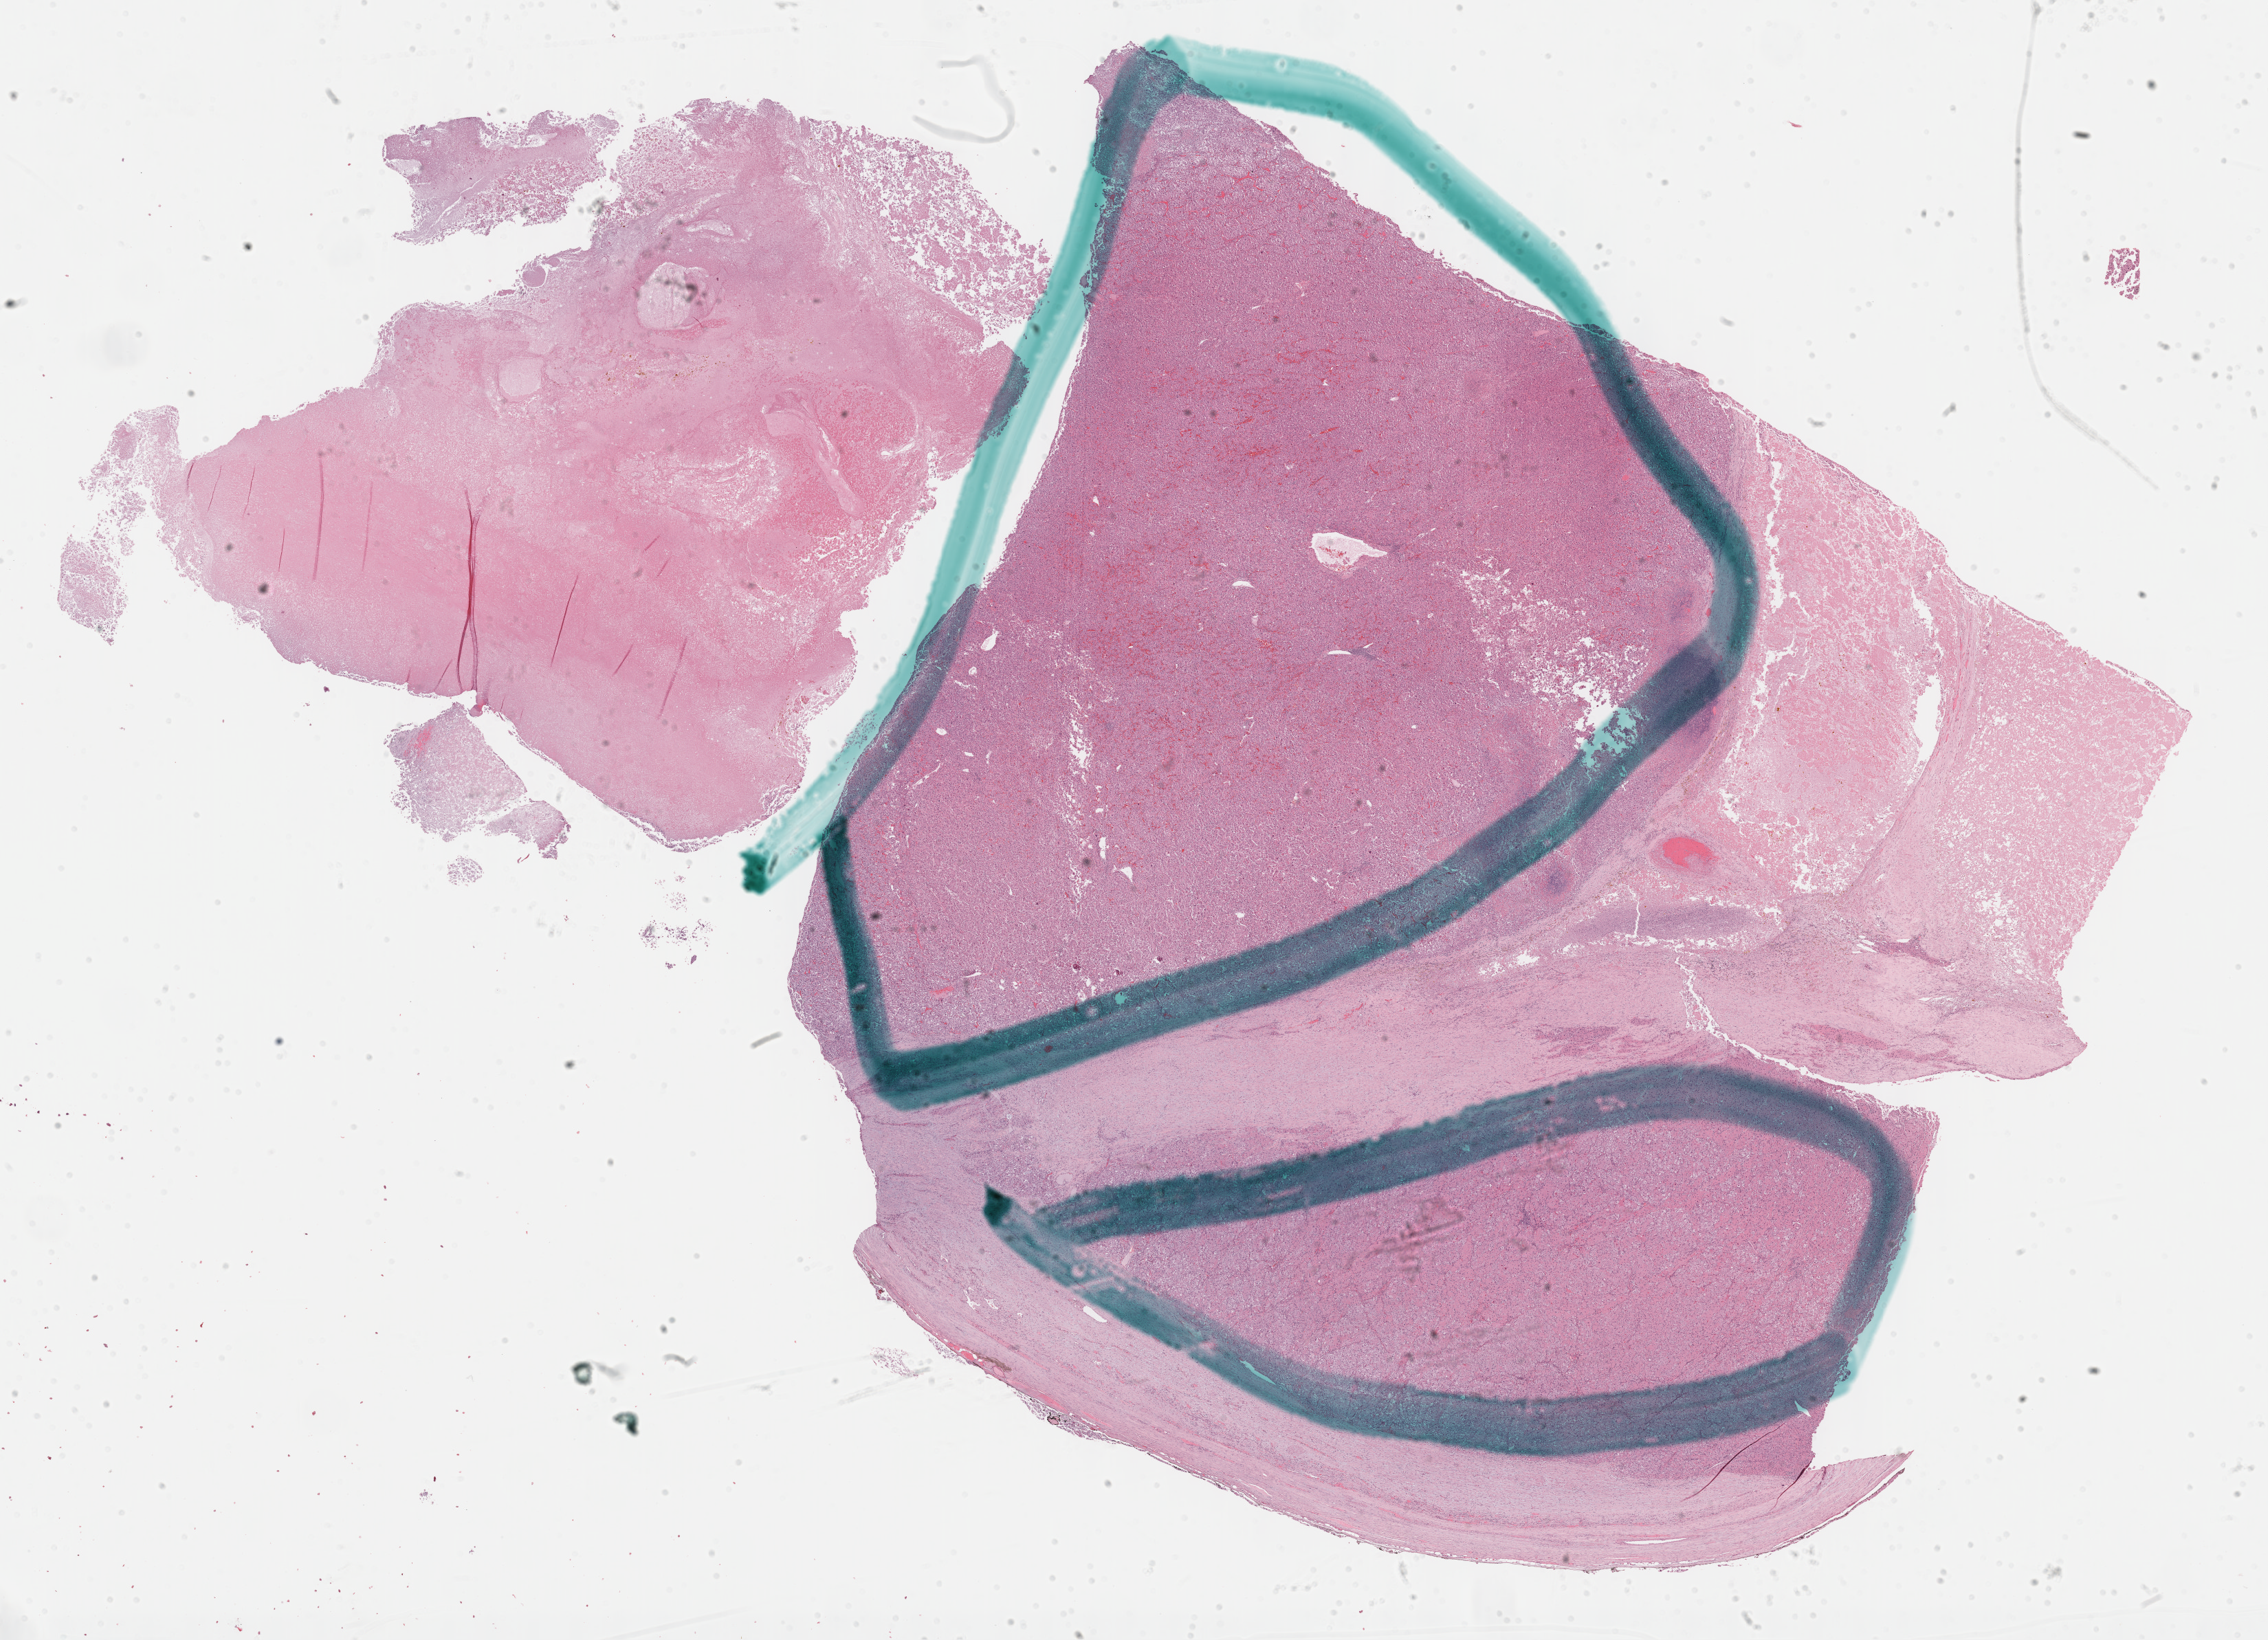
Digitized H&E-stained tissue section (whole slide), shown as a low-resolution overview of the whole scanned area (about 26.7 x 19.3 mm, slide scanned at 40x). FFPE section. Sample: primary tumour, adrenal cortex. Male, age 55 years at initial diagnosis.
Pathologic diagnosis: Adrenal cortical carcinoma (cortex of adrenal gland).